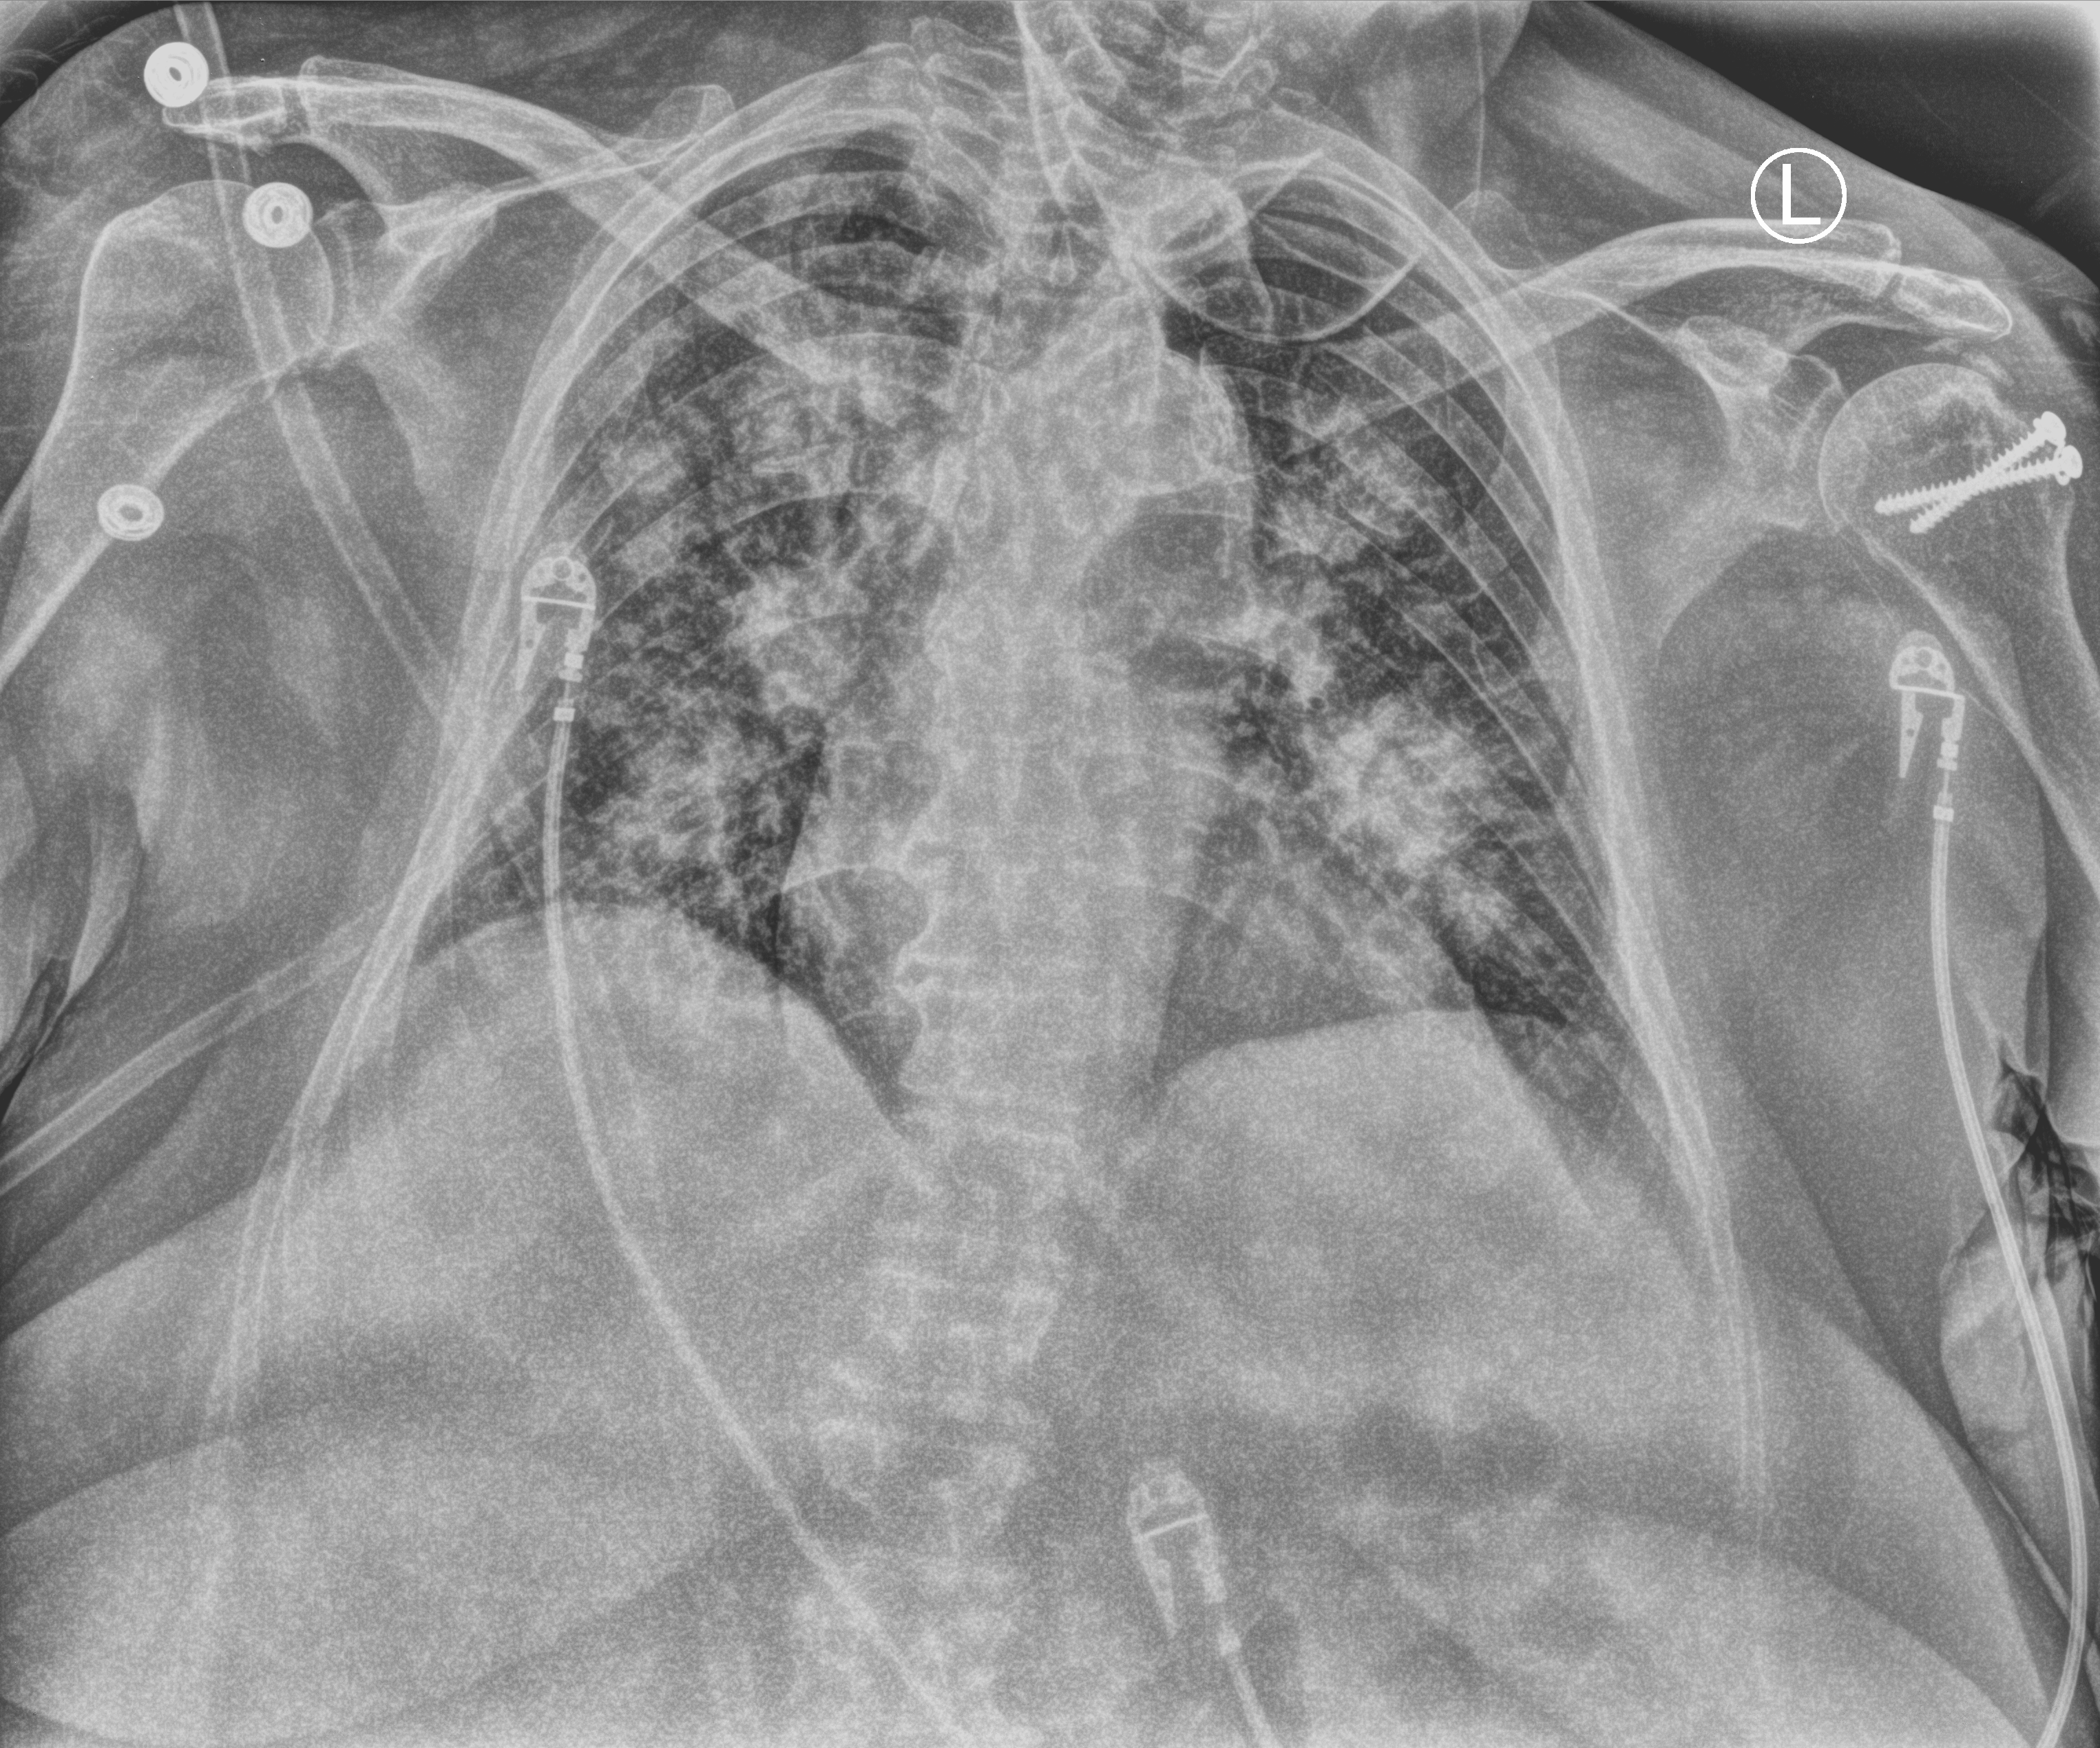
Chest X-ray (portable); anteroposterior (AP) projection. Patient hospitalised with COVID-19; female, aged 60–74 years.
From the hospital-stay record, not from the radiograph (when in the stay this image was taken is not recorded): diabetes (admission record): yes.